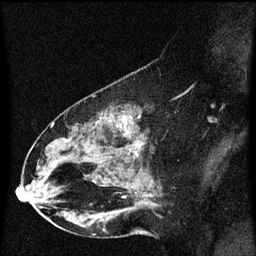
Breast MRI (dynamic contrast-enhanced), one sagittal slice. Dynamic contrast-enhanced series, image 2 of 3 at this slice position (ordered by acquisition). 1.5 T. TE 4.2 ms, TR 8.4 ms. 2 mm slice thickness. 256 × 256 image matrix, field of view 200 × 200 mm. Patient: female, 49 years. From the clinical record (not read from this slice): setting: breast cancer imaged before/during neoadjuvant chemotherapy; receptor status: HR-positive, HER2-negative.
Outlined on this slice (semi-automatic segmentation, software-assisted and operator-edited):
- analysis volume of interest (the breast-tissue region the enhancement analysis was run in; not a lesion): box from (x=27, y=96) to (x=164, y=221) px
- tumour enhancement mask (voxels above the 70 % enhancement threshold inside the analysis volume of interest): (x=121, y=122)–(x=139, y=155)